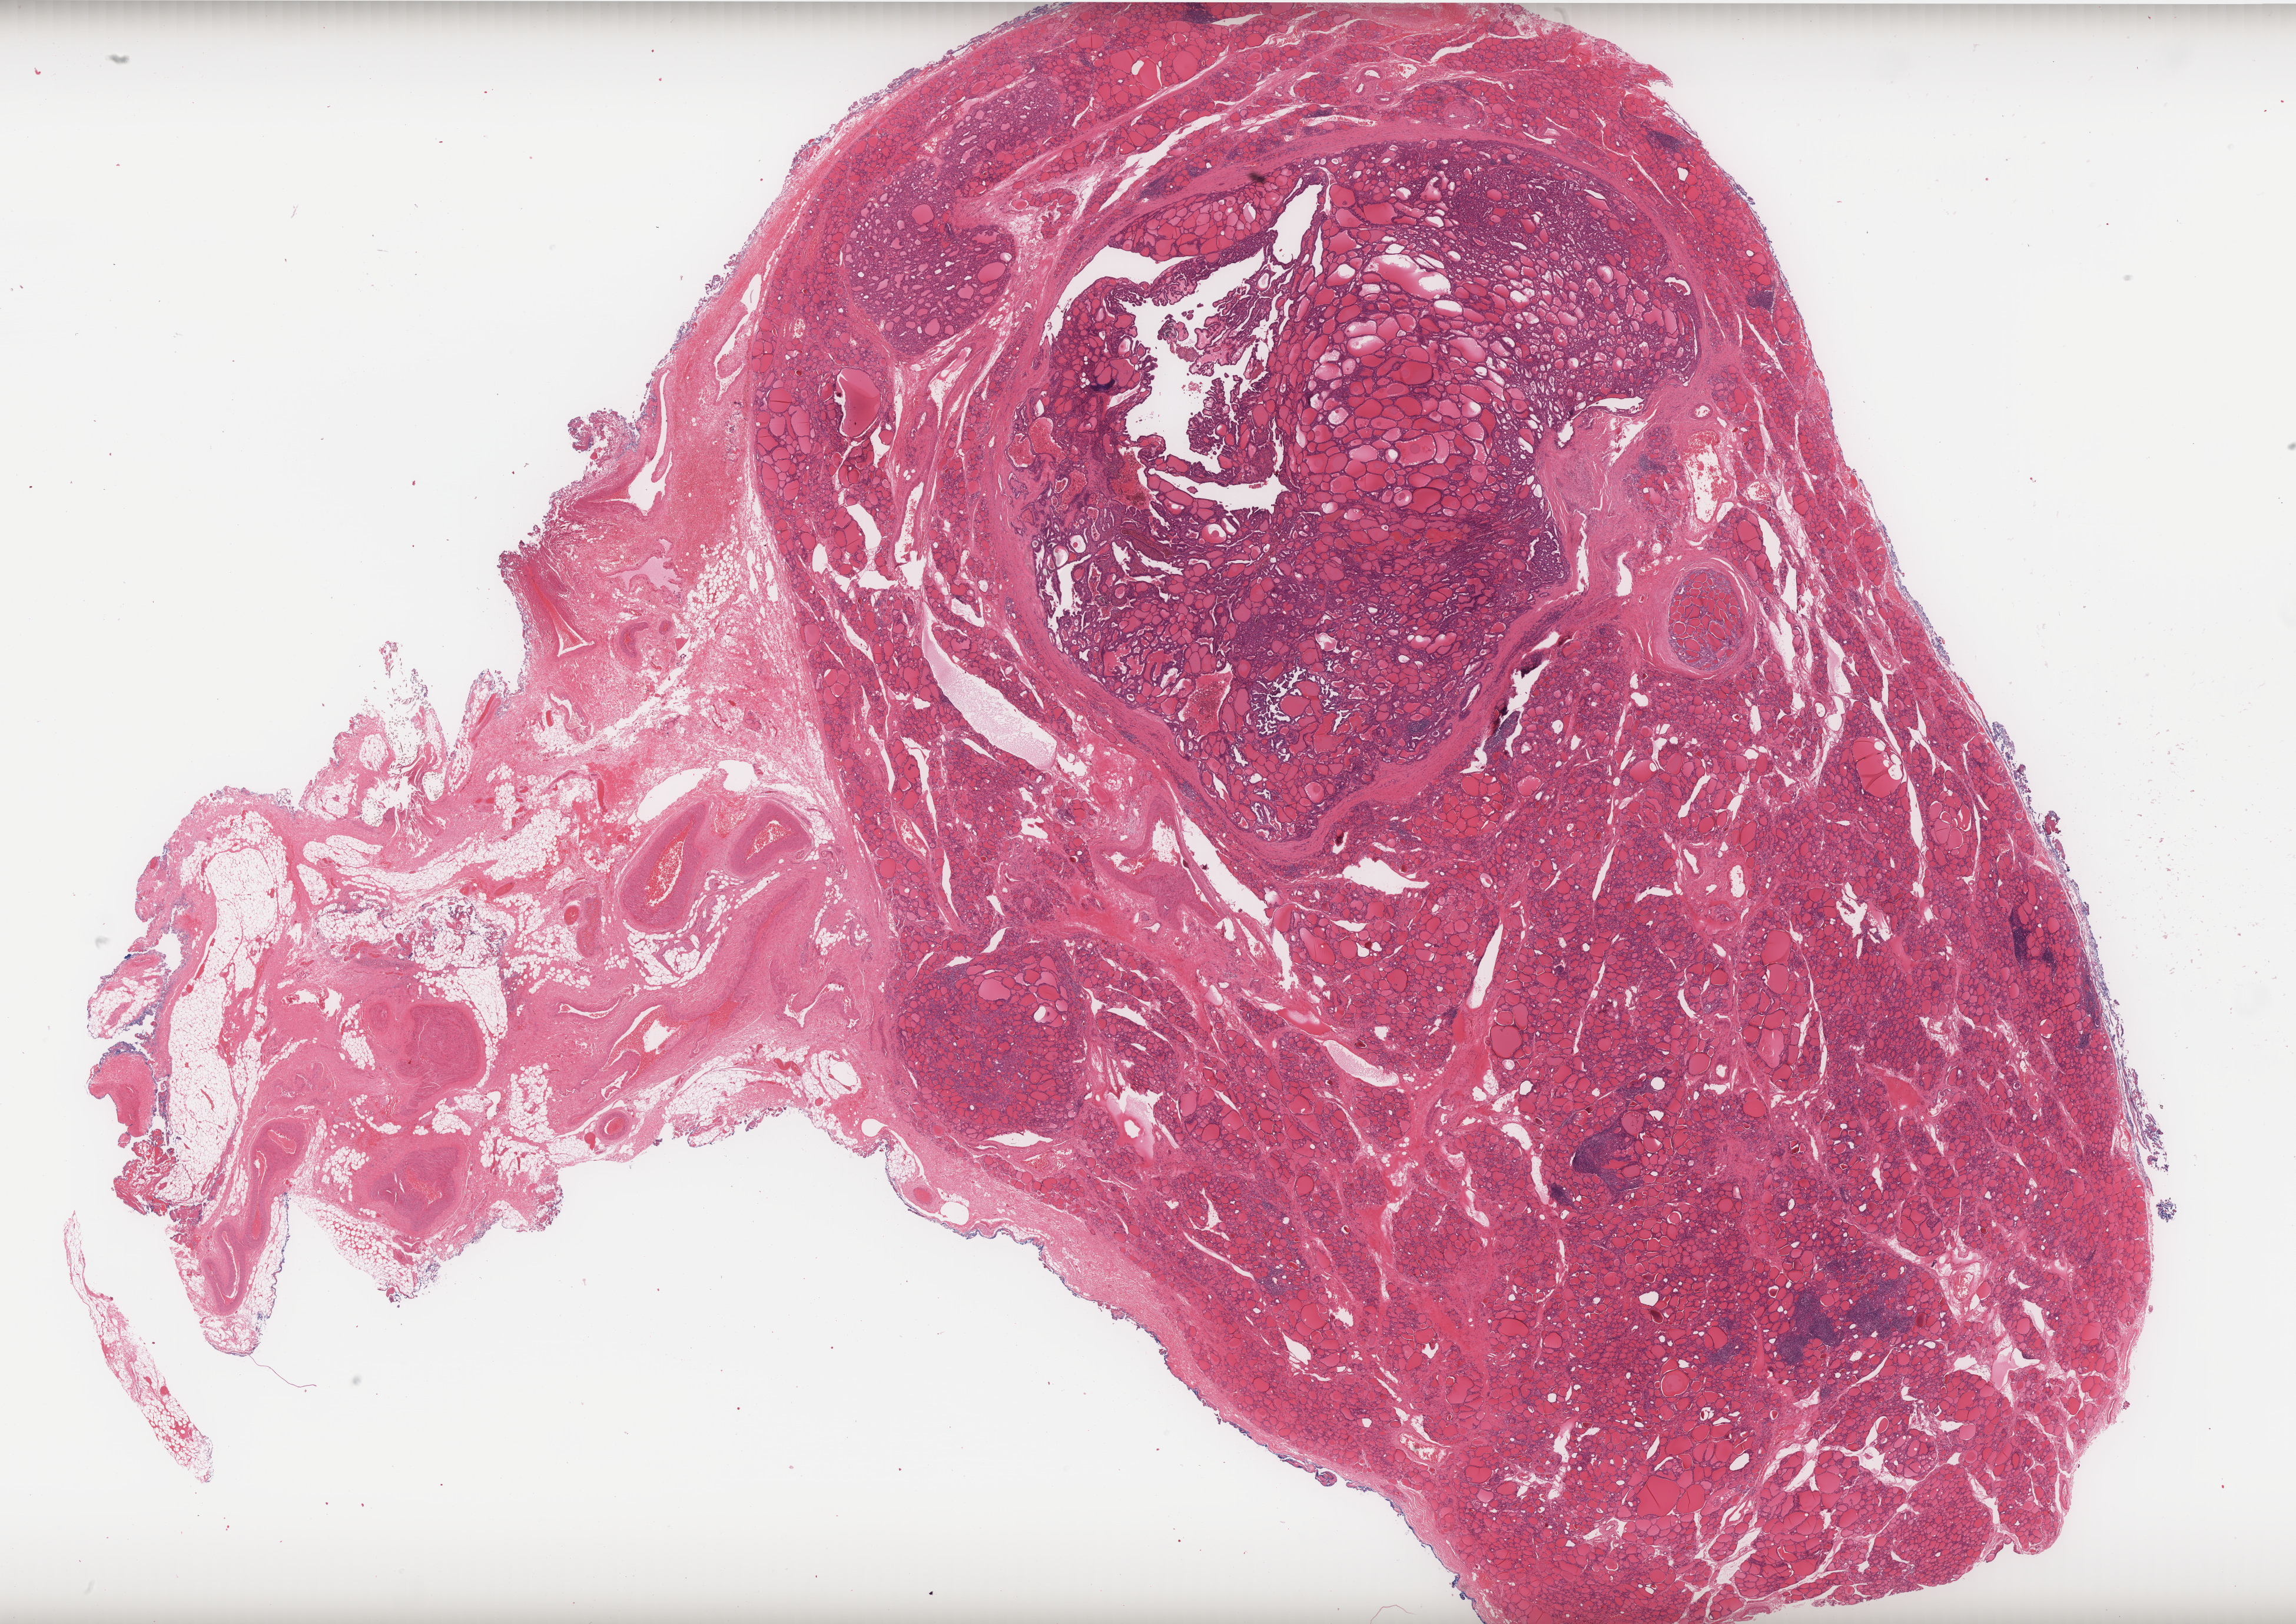
H&E whole-slide image, shown as a low-resolution overview of the whole scanned area (about 31.3 x 22.1 mm, from a 40x scan), formalin-fixed paraffin-embedded (FFPE) diagnostic section, sample: primary tumour, thyroid. Female, age 55 years at initial diagnosis.
- AJCC pathologic stage: I
- diagnosis: Papillary adenocarcinoma, NOS (thyroid gland)
- lymph nodes positive (case pathology): 0 of 6 examined